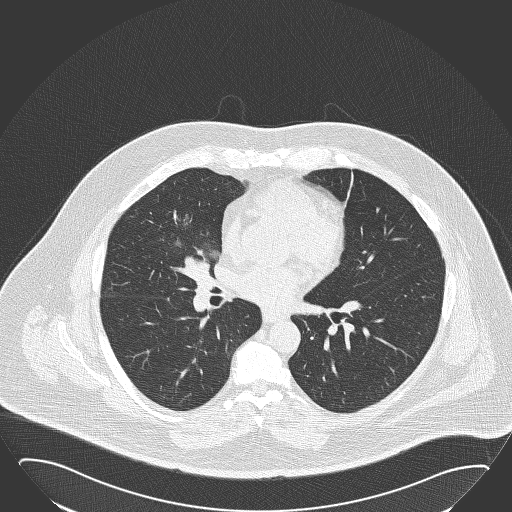
Low-dose screening chest CT, one axial slice; position 81 of 168 along the scan axis; reconstruction kernel B50f; 120 kVp; lung window (W 1500 / L -600 HU); 2 mm slice thickness; 512 × 512 image matrix, field of view 432 × 432 mm.
Outlined on this slice (outlined manually by an expert reader):
- lesion 1 (tumor, hilum of right lung): box from (x=175, y=257) to (x=210, y=285) px